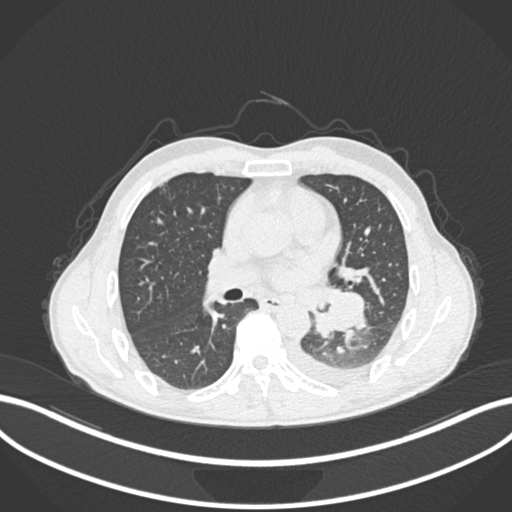
Chest CT, one axial slice. Slice 130 of 222 in the series (ordered by position). Reconstruction kernel B30f. 120 kVp. Lung window (W 1500 / L -600 HU). 1 mm slice thickness. 512 × 512 image matrix. Patient: male, 47 years. From the clinical record (not read from this slice): clinical TNM (as recorded): T3 N1 M1c; histopathological grade: G3.
Annotated regions visible in this slice (bounding box drawn by a radiologist):
- lung tumour (recorded histology: small cell carcinoma): bounding box (x1, y1, x2, y2) in pixels: (309, 284, 367, 339)